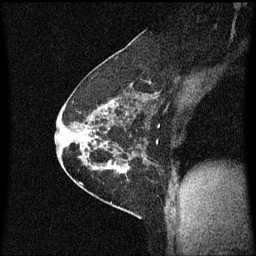
Breast MRI (dynamic contrast-enhanced), one sagittal slice; slice 39 of 60 in the series (ordered by position); dynamic contrast-enhanced series, image 2 of 3 at this slice position (ordered by acquisition); 1.5 T; TE 4.2 ms, TR 8.4 ms; 2 mm slice thickness; 256 × 256 image matrix, field of view 200 × 200 mm. Female patient, age 60 years.
Structures marked on this image (semi-automatically segmented with operator editing):
- analysis volume of interest (the breast-tissue region the enhancement analysis was run in; not a lesion): bounding box [x1, y1, x2, y2] px = [69, 66, 149, 193]
- tumour enhancement mask (voxels above the 70 % enhancement threshold inside the analysis volume of interest): [69, 94, 147, 173]